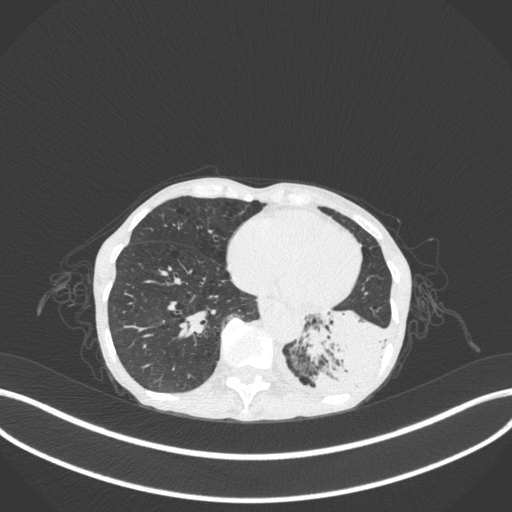
Chest CT, one axial slice; position 68 of 347 along the scan axis; reconstruction kernel B31f; 120 kVp; lung window (W 1500 / L -600 HU); 1 mm slice thickness; 512 × 512 image matrix, field of view 400 × 400 mm. Patient: female, 70 years. From the clinical record (not read from this slice): clinical TNM (as recorded): T3 N0 M0.
Annotated regions visible in this slice (rectangle marked by the reading radiologist):
- lung tumour (recorded histology: small cell carcinoma): bounding box <301,300,388,403> (left, top, right, bottom; pixels)